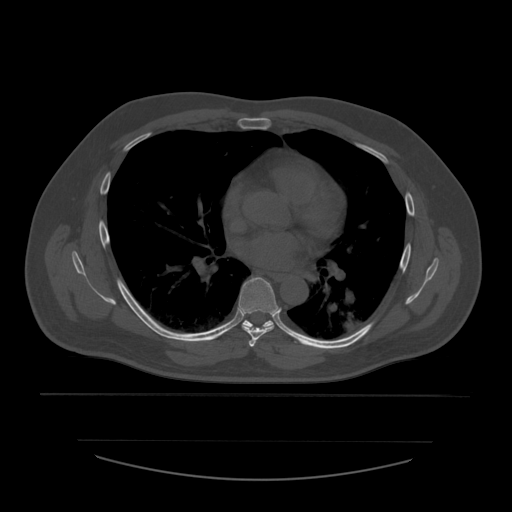
CT including the spine, one axial slice; reconstruction kernel STANDARD; bone window (W 1800 / L 400 HU); 512 × 512 image matrix, field of view 441 × 441 mm. Patient age 44 years. Case-level facts recorded for this patient, not image findings: primary cancer: soft tissue sarcoma.
Outlined on this slice (semi-automatic segmentation, software-assisted and operator-edited):
- T5 vertebra: box from (x=249, y=339) to (x=257, y=347) px
- T6 vertebra: (x=239, y=278)–(x=279, y=341)
- T7 vertebra: (x=243, y=320)–(x=274, y=328)